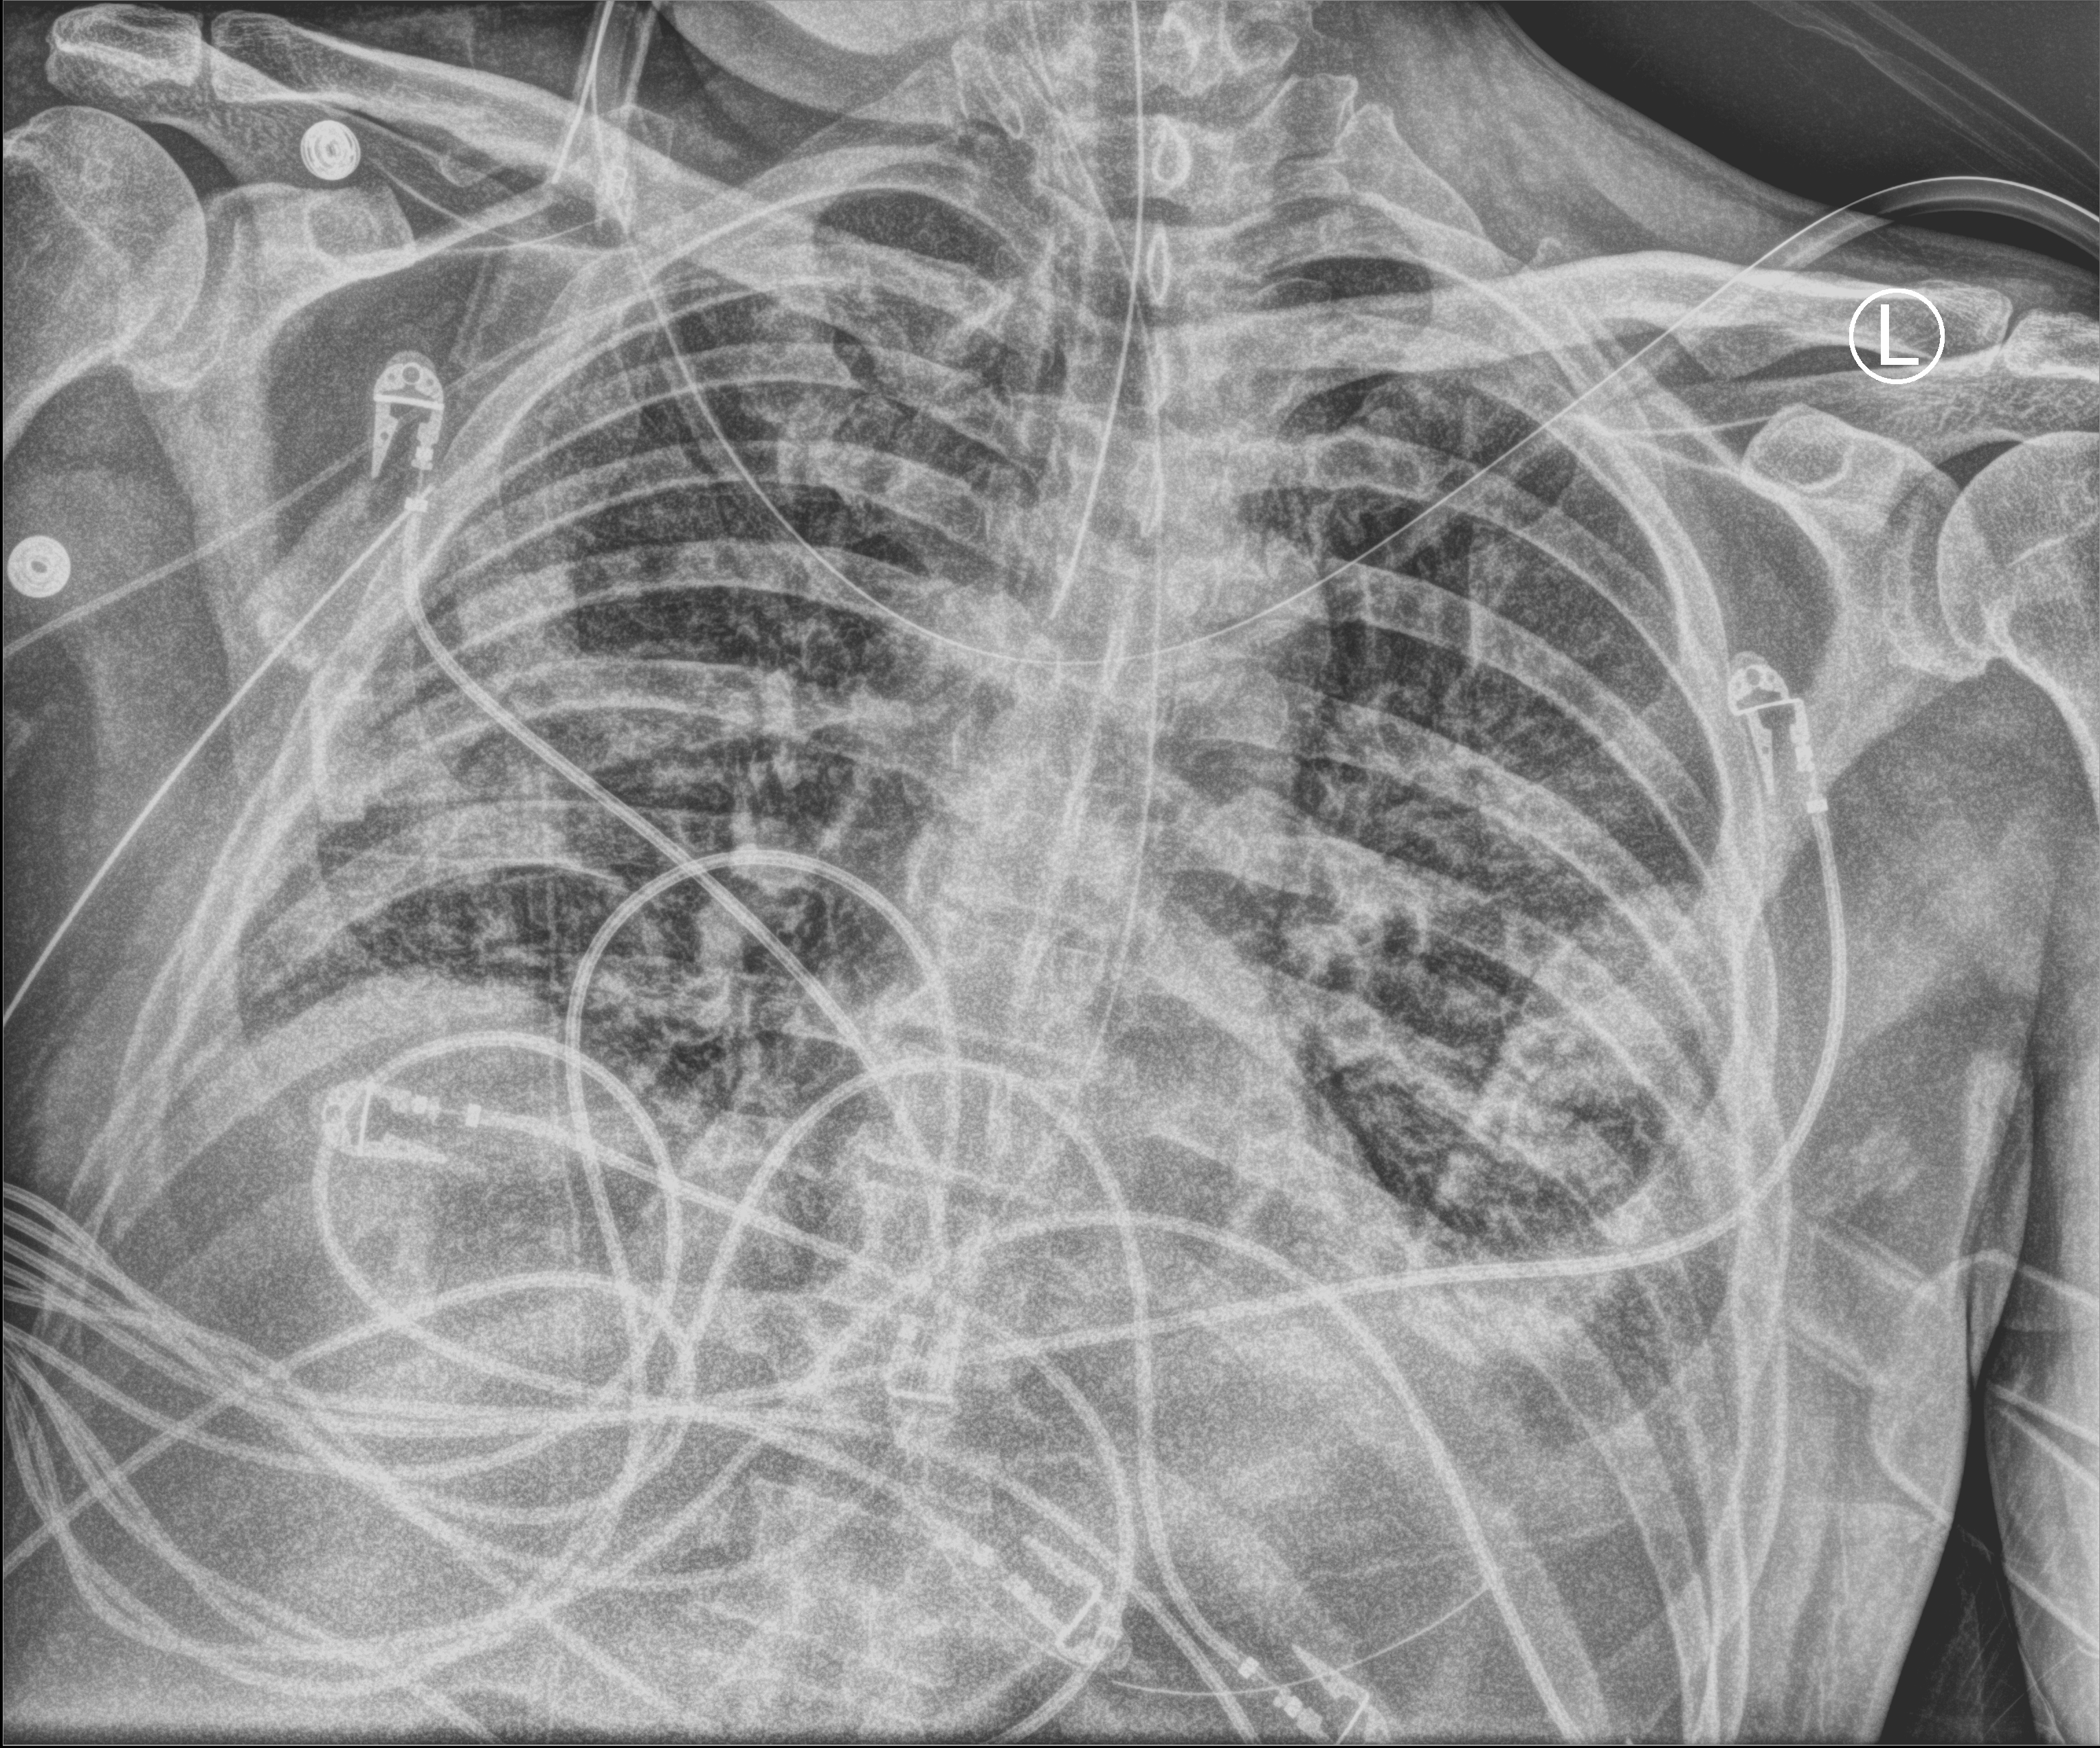
Portable chest radiograph, anteroposterior (AP) projection. Patient hospitalised with COVID-19; male, aged 60–74 years.
Admission-level facts for this patient (not findings on this image; timing relative to this image not recorded): admitted to intensive care during this hospital stay: yes; mechanically ventilated during this hospital stay: yes.